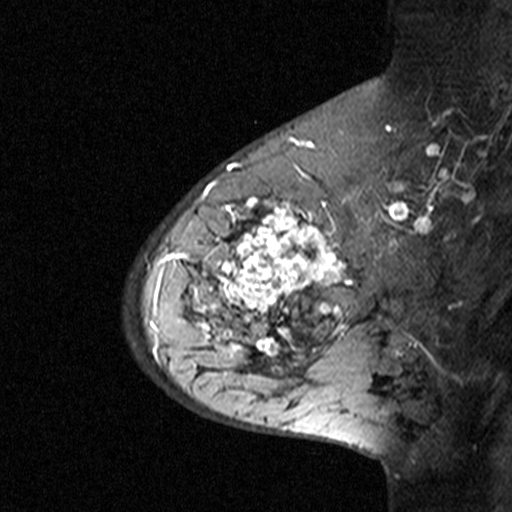
Breast MRI (dynamic contrast-enhanced), one sagittal slice. Slice 28 of 44 in the series (ordered by position). Dynamic contrast-enhanced study with each time point stored as its own series, time point 3 of 4 at this slice position (ordered by acquisition time). 1.5 T. TE 4.5 ms, TR 11 ms. 3 mm slice thickness. 512 × 512 image matrix, field of view 200 × 200 mm. Female patient, age 65 years. Case-level facts recorded for this patient, not image findings: setting: breast cancer imaged before/during neoadjuvant chemotherapy; receptor status: HER2-positive.
Structures marked on this image (semi-automatic segmentation, software-assisted and operator-edited):
- analysis volume of interest (the breast-tissue region the enhancement analysis was run in; not a lesion): bounding box <182,190,353,361> (left, top, right, bottom; pixels)
- tumour enhancement mask (voxels above the 90 % enhancement threshold inside the analysis volume of interest): <182,190,351,356>